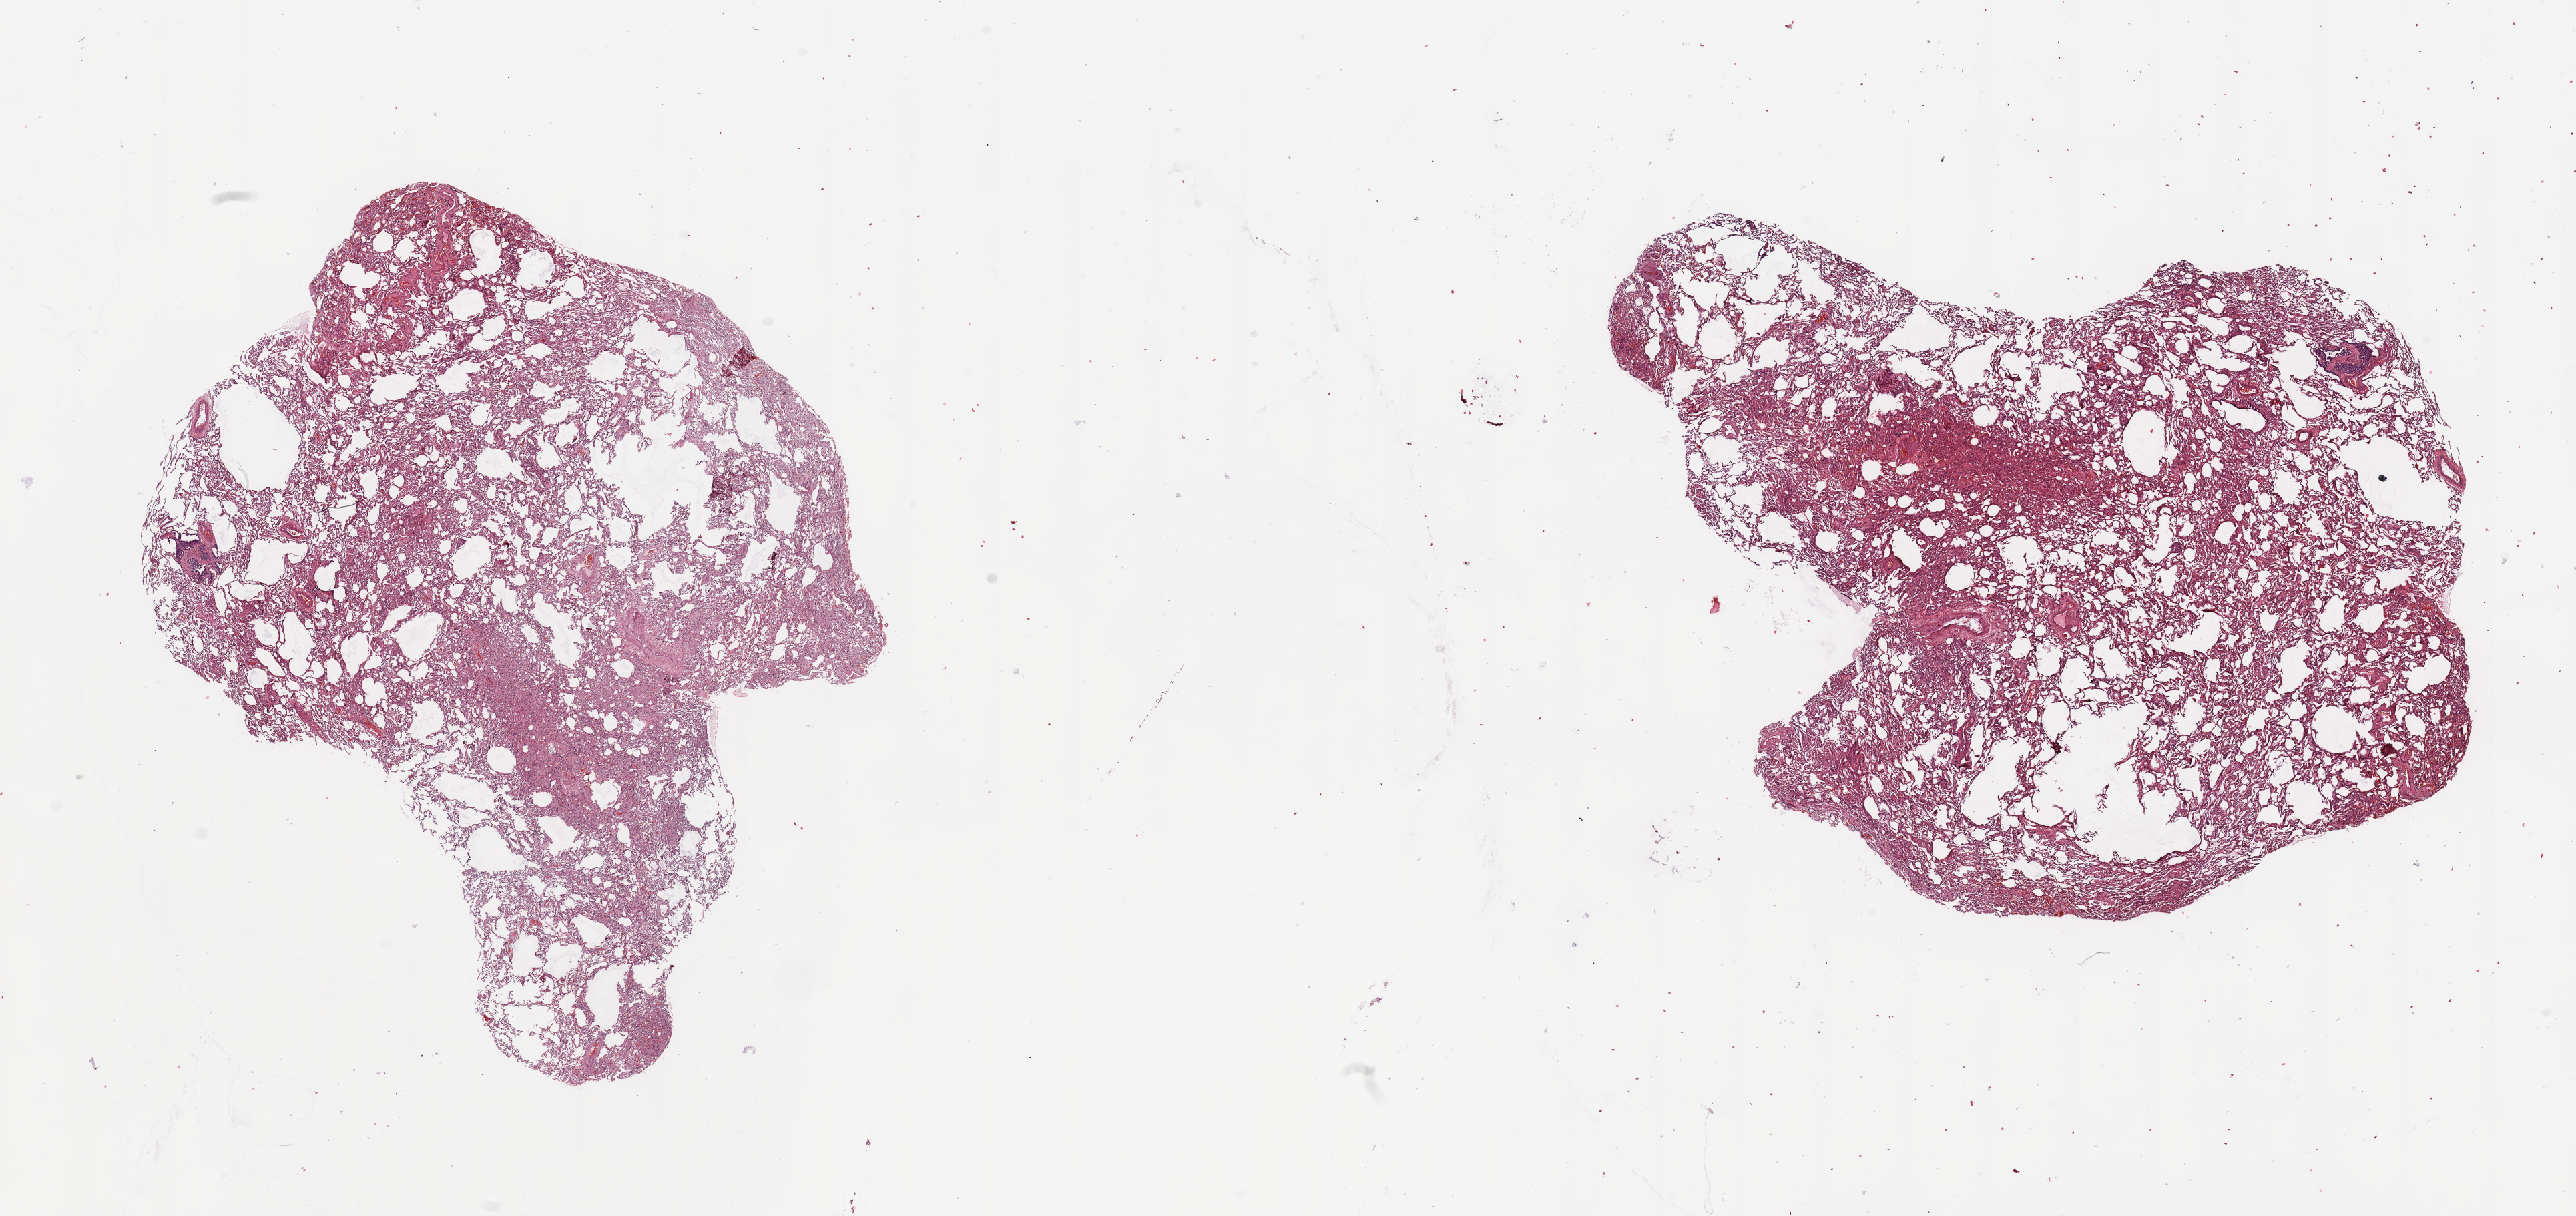
Whole-slide histology image, Hematoxylin and eosin (H&E) stained, shown as a low-resolution overview of the whole scanned area (about 30.5 x 14.4 mm, slide scanned at 20x), normal (non-tumour) tissue sample, lung. Patient: female, age 67 years.
This section: normal (non-tumour) tissue from the same patient. Patient diagnosis: Adenocarcinoma, NOS.